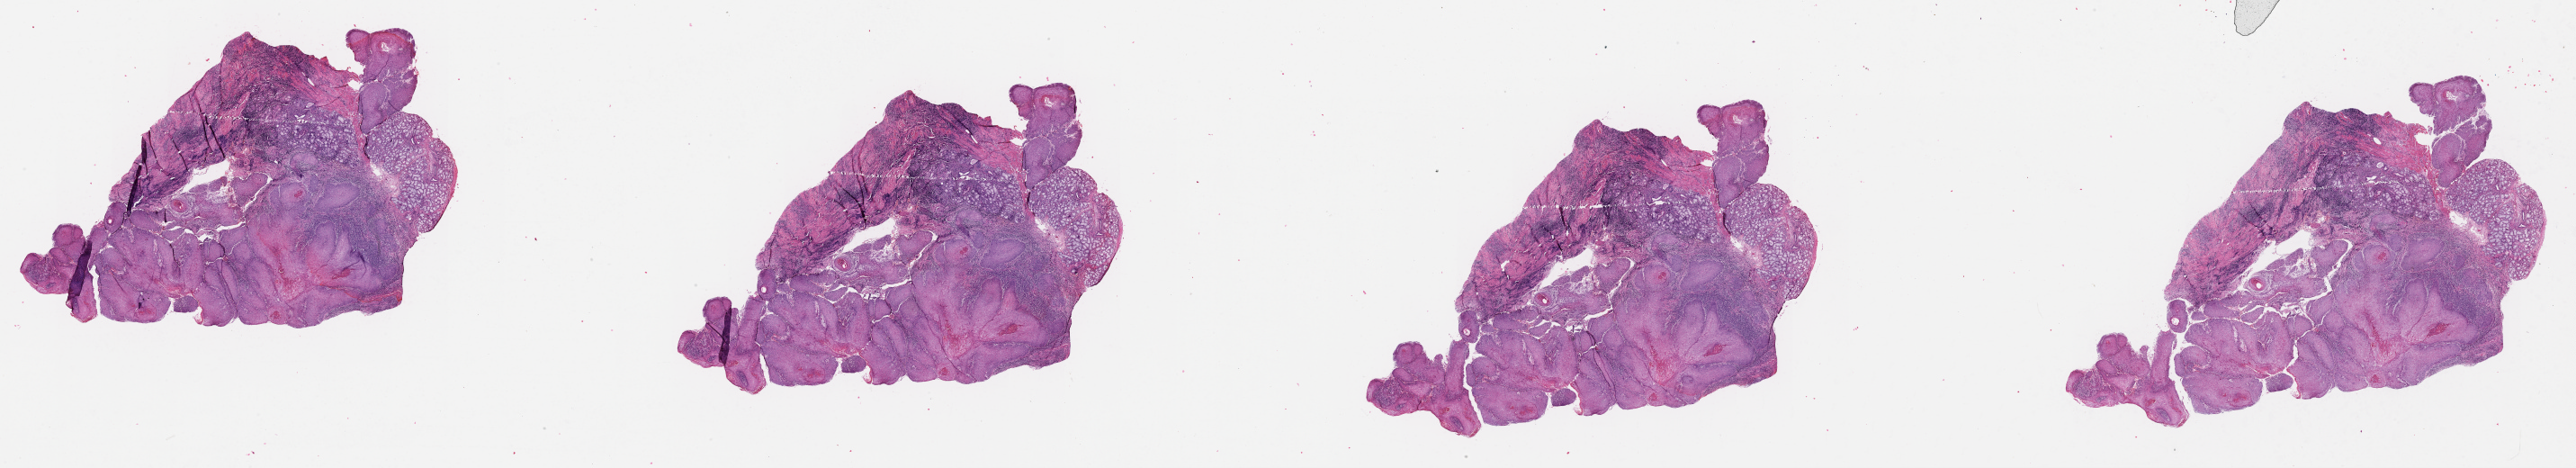
Whole-slide histology image, H&E-stained — low-resolution overview of the scanned area, about 46.1 x 8.4 mm (from a 20x scan); head and neck, tissue type not recorded. Patient: male, age 69 years.
- patient diagnosis: Squamous cell carcinoma, NOS